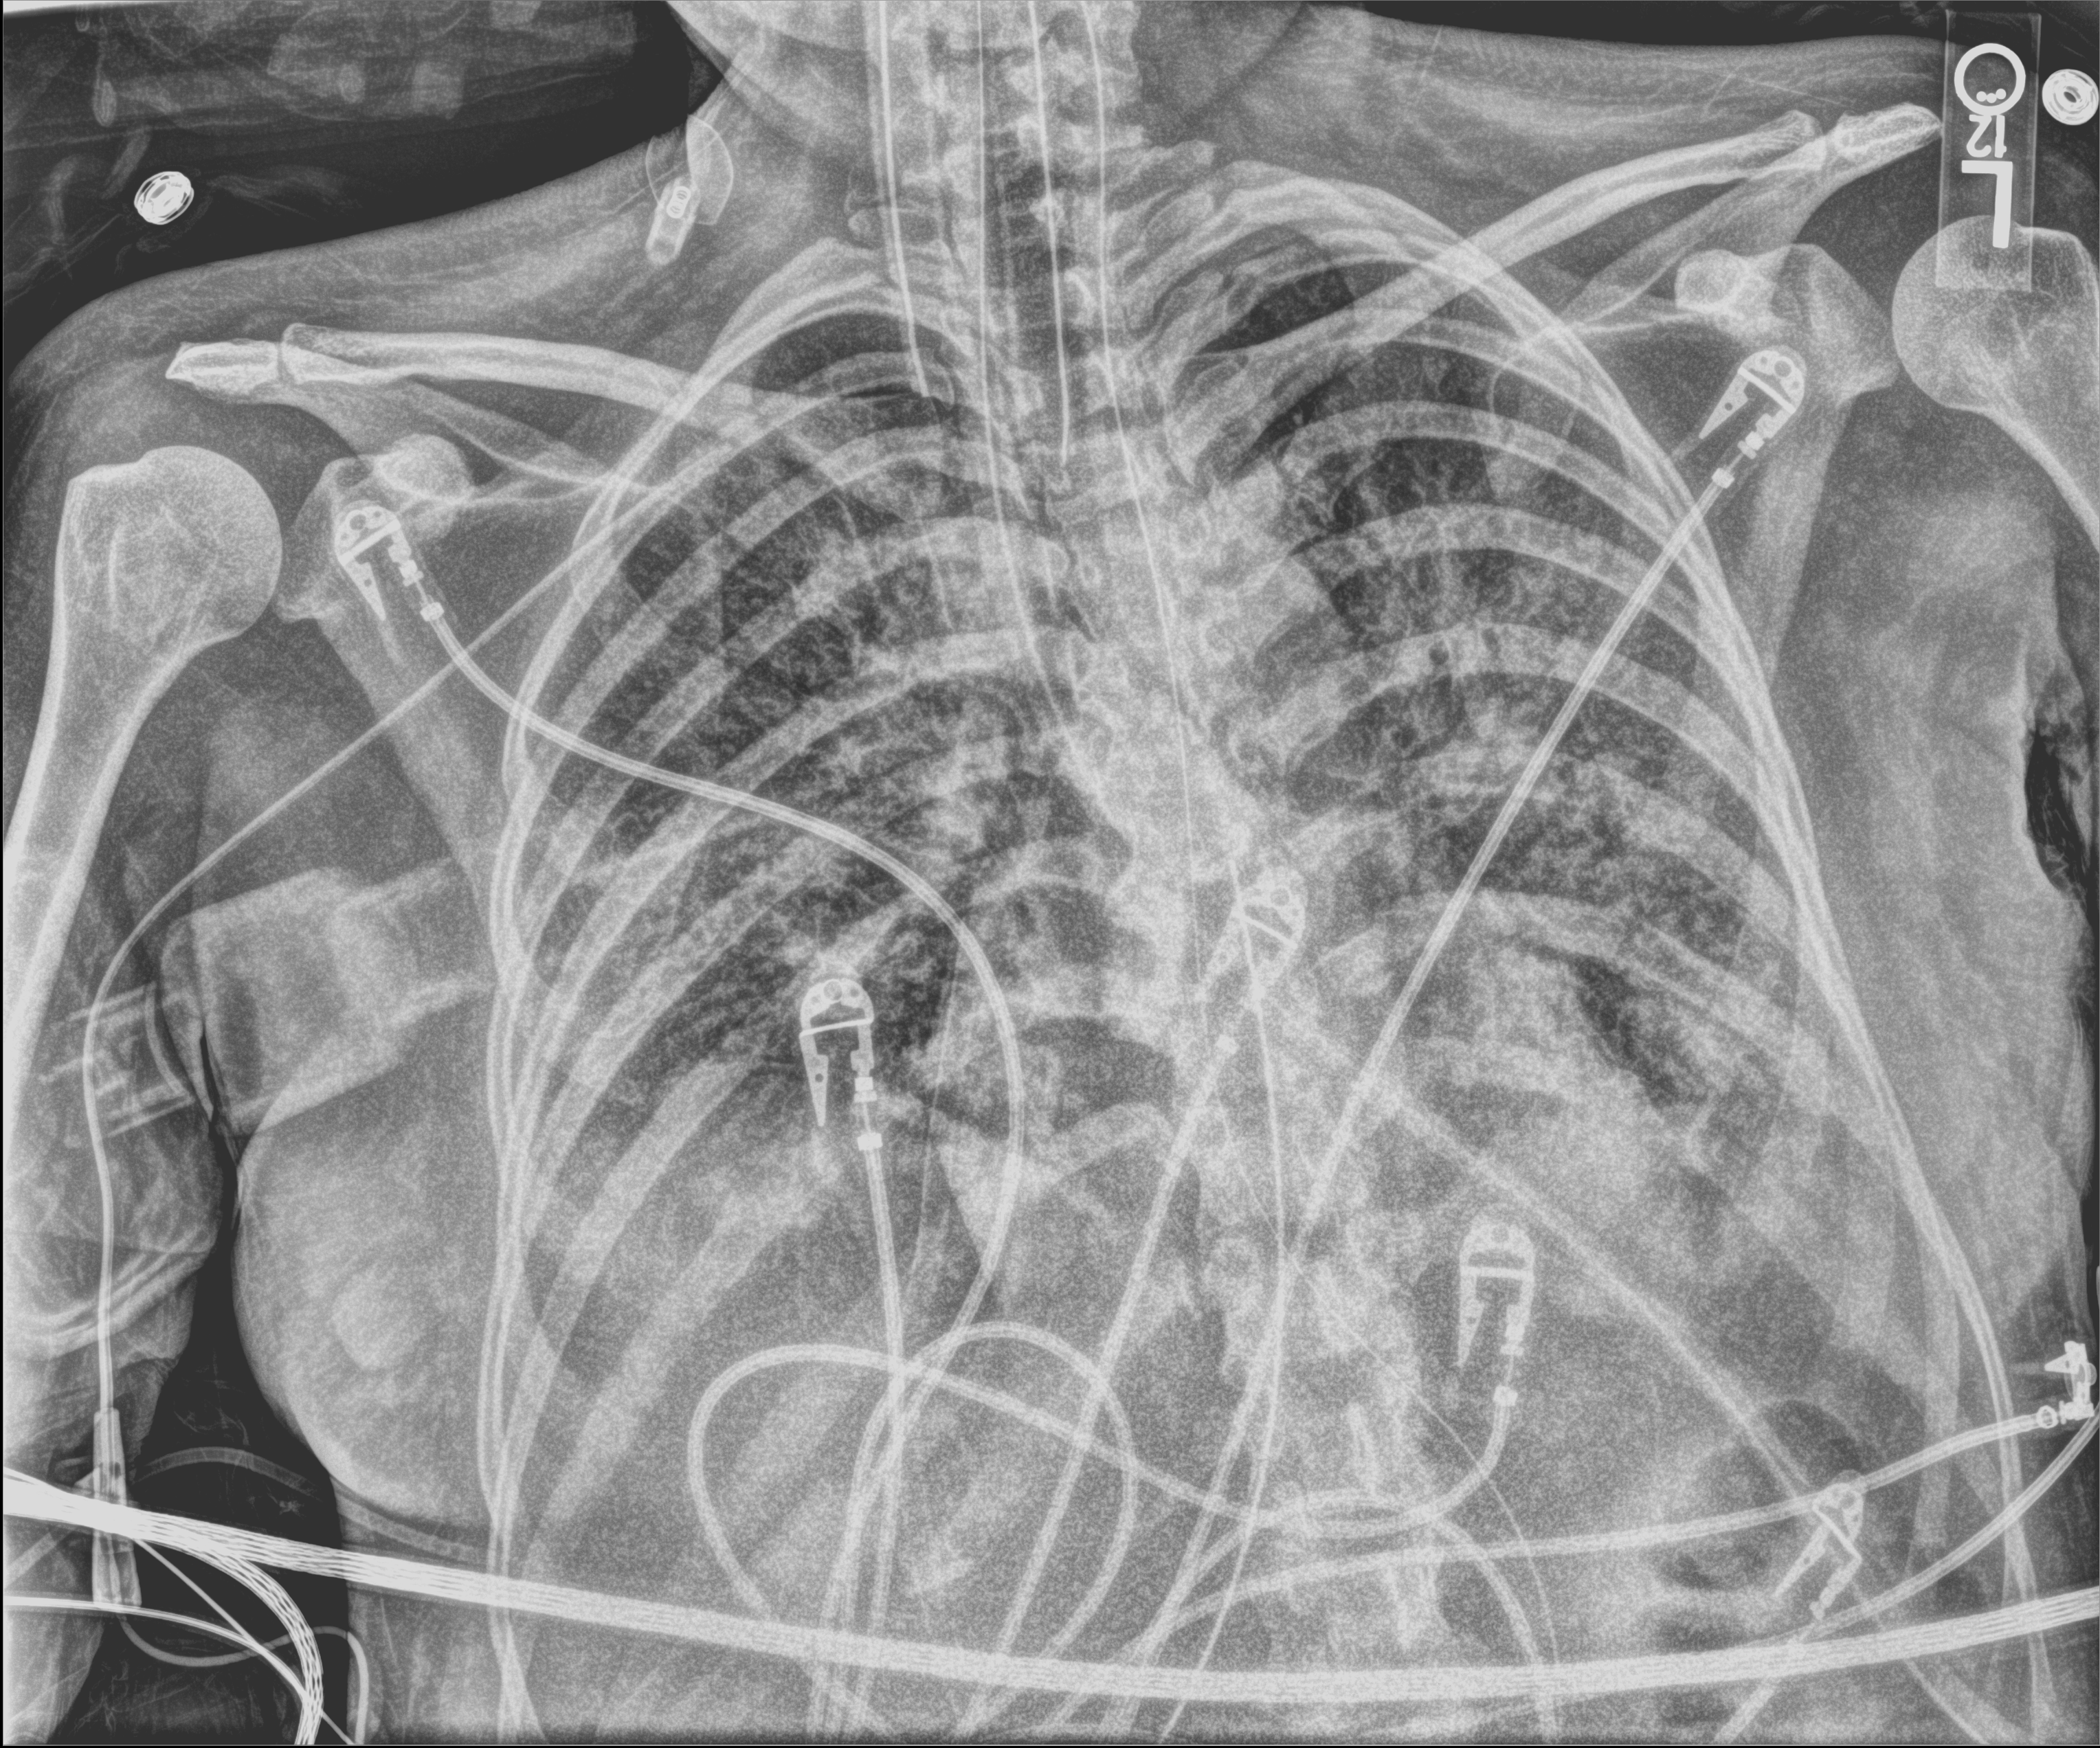
Bedside chest radiograph (computed radiography), anteroposterior (AP) projection. Patient hospitalised with COVID-19; female, aged 18–59 years.
Admission-level facts for this patient (not findings on this image; timing relative to this image not recorded): length of hospital stay: 71 days.